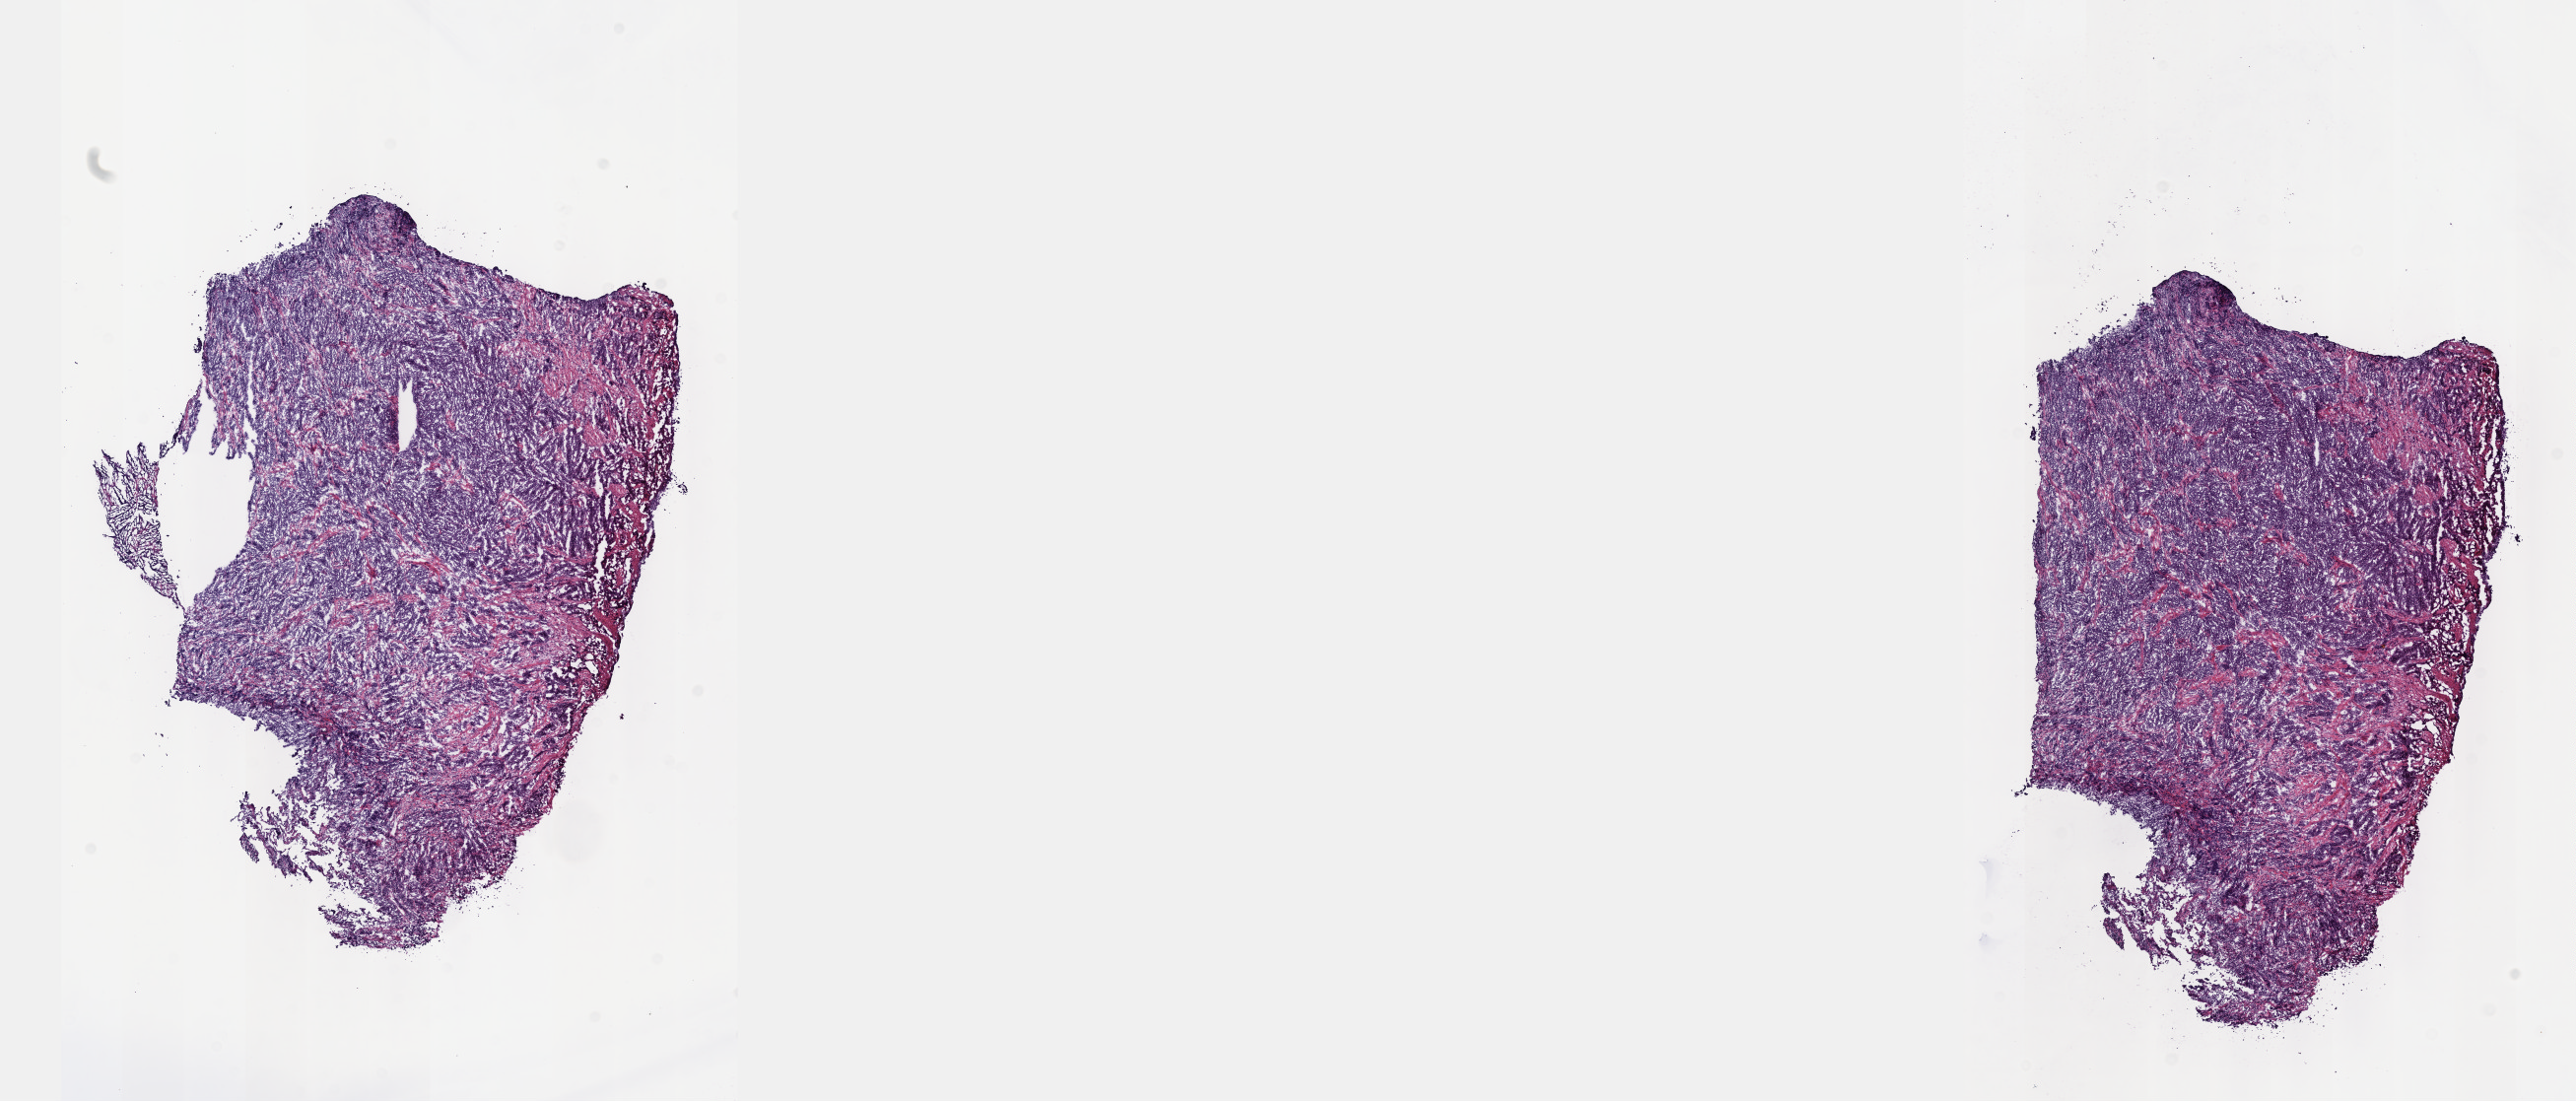
Digitized H&E-stained tissue section (whole slide) — a low-resolution overview of the entire scanned area, about 21.1 x 9.0 mm (slide scanned at 40x); frozen section; thymus, primary tumour sample. Patient: female, age at initial diagnosis 78 years. Slide review estimates, as recorded: tumour cells 70%, tumour nuclei 90%, normal cells 0%, stromal cells 30%, necrosis 0%. Inflammatory infiltration, as recorded: lymphocyte infiltration 0%, monocyte infiltration 0%, neutrophil infiltration 0%.
Histologic diagnosis: Thymic carcinoma, NOS.